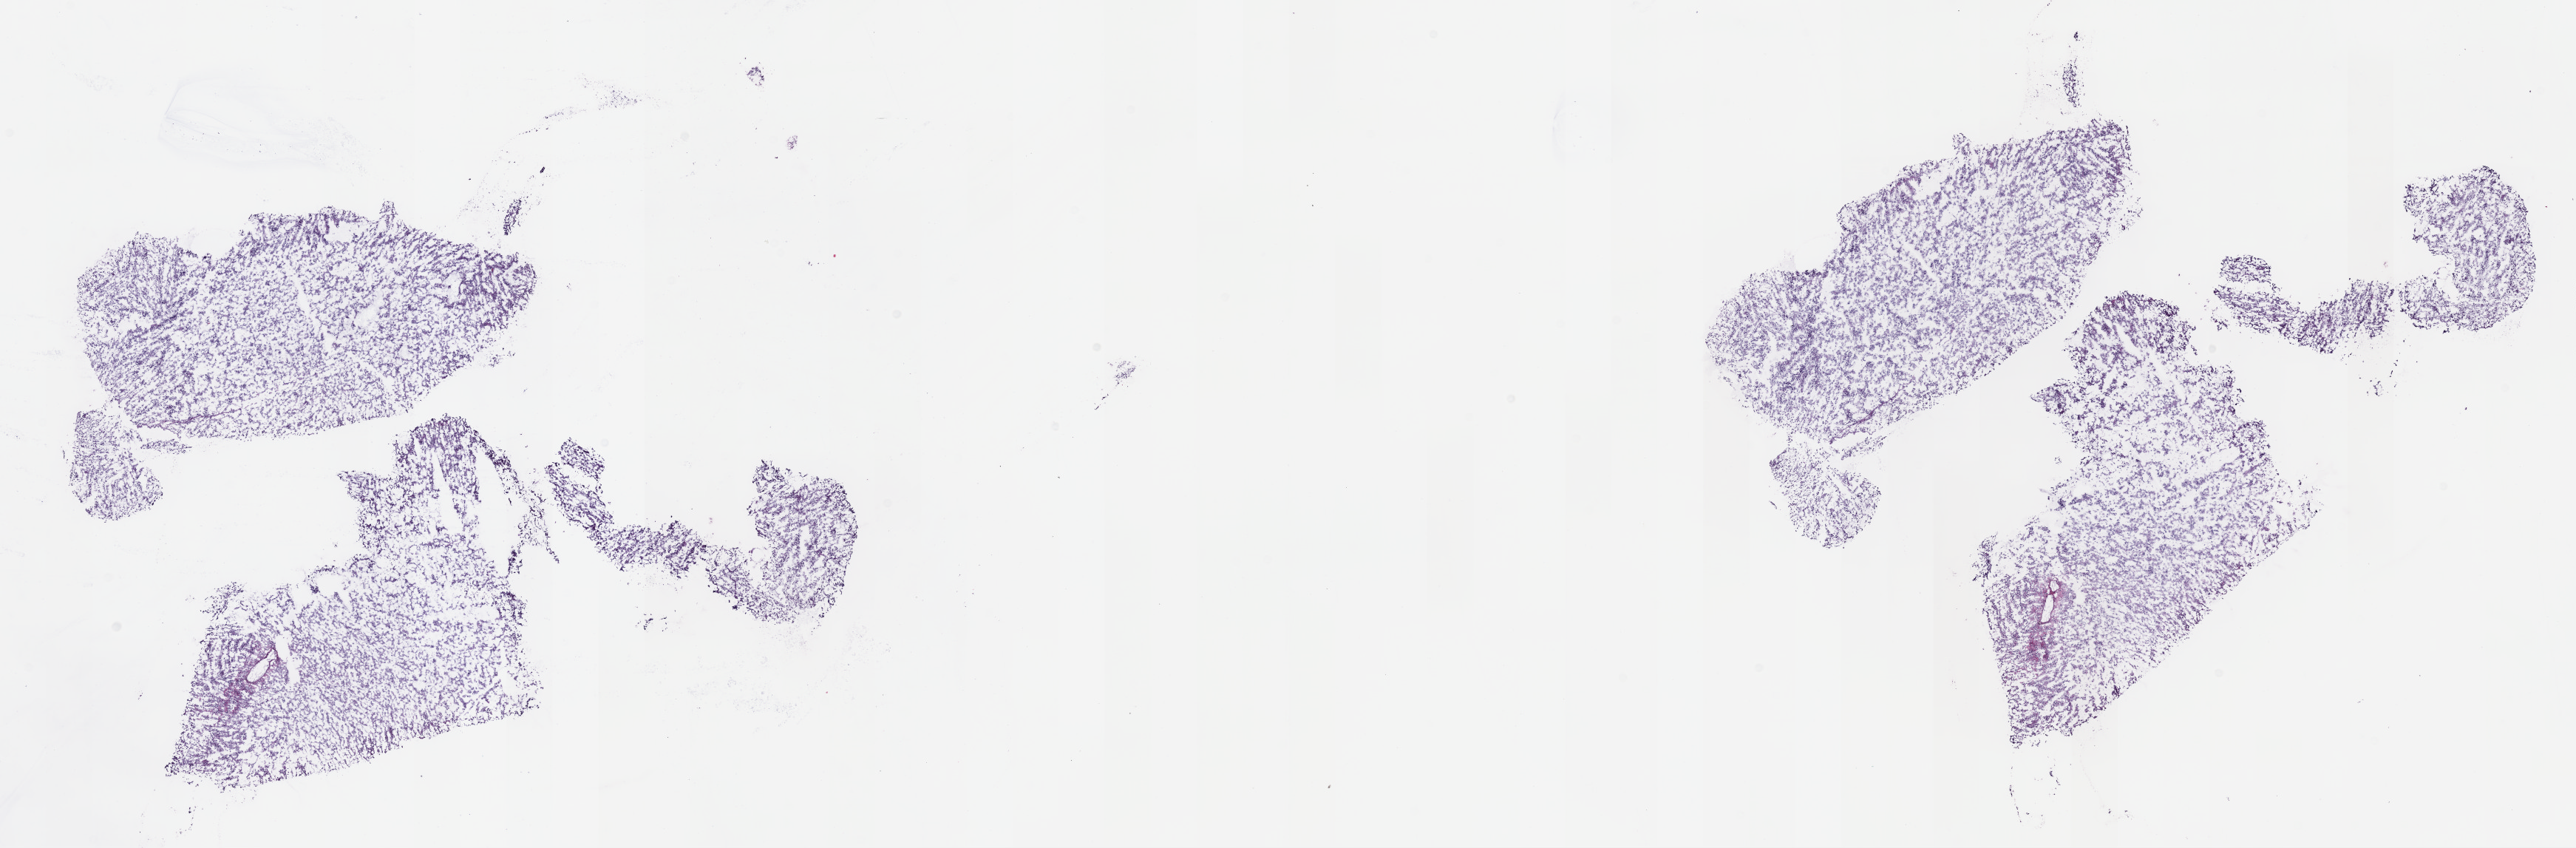
Hematoxylin and eosin (H&E) stained whole-slide image — low-resolution overview of the scanned area, about 28.2 x 9.3 mm (acquisition: 40x scan); frozen section from the top of the tissue portion; brain, primary tumour sample. Female, age 42 years at initial diagnosis. Histologic grade: G2 (moderately differentiated). Slide review estimates, as recorded: tumour cells 80%, tumour nuclei 90%, normal cells 10%, stromal cells 10%, necrosis 0%. Inflammatory infiltration, as recorded: lymphocyte infiltration 0%, monocyte infiltration 0%, neutrophil infiltration 0%.
Histologic diagnosis: Oligodendroglioma, NOS (cerebrum).